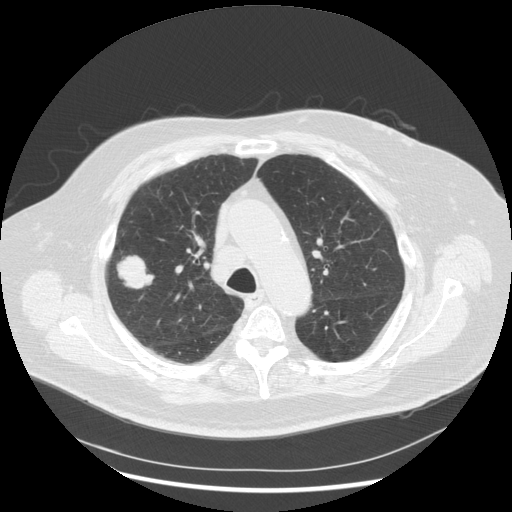
Chest CT (low-dose screening protocol), one axial image, third screening round (two years after baseline), lung window (W 1500 / L -600 HU), standard (soft-tissue) reconstruction kernel (STANDARD), 120 kVp, slice 197 of 263 in the series, 512 × 512 image matrix, field of view 400 × 400 mm. Male, age 72 years at enrolment. Former smoker at enrolment.
Expert reader's lesion annotation, box from (x=106, y=251) to (x=161, y=300) px. Reader record for this screening exam (exam-level; its link to the box is not recorded): non-calcified nodule or mass ≥4 mm, right upper lobe, 31 × 31 mm, poorly defined margins, soft tissue attenuation, pre-existing on the prior screen: no. Later outcome: lung cancer diagnosed 70 days after this screen — squamous cell carcinoma, NOS, right upper lobe, poorly differentiated (G3), stage IIIA (AJCC 6th edition), 19 mm at pathology.